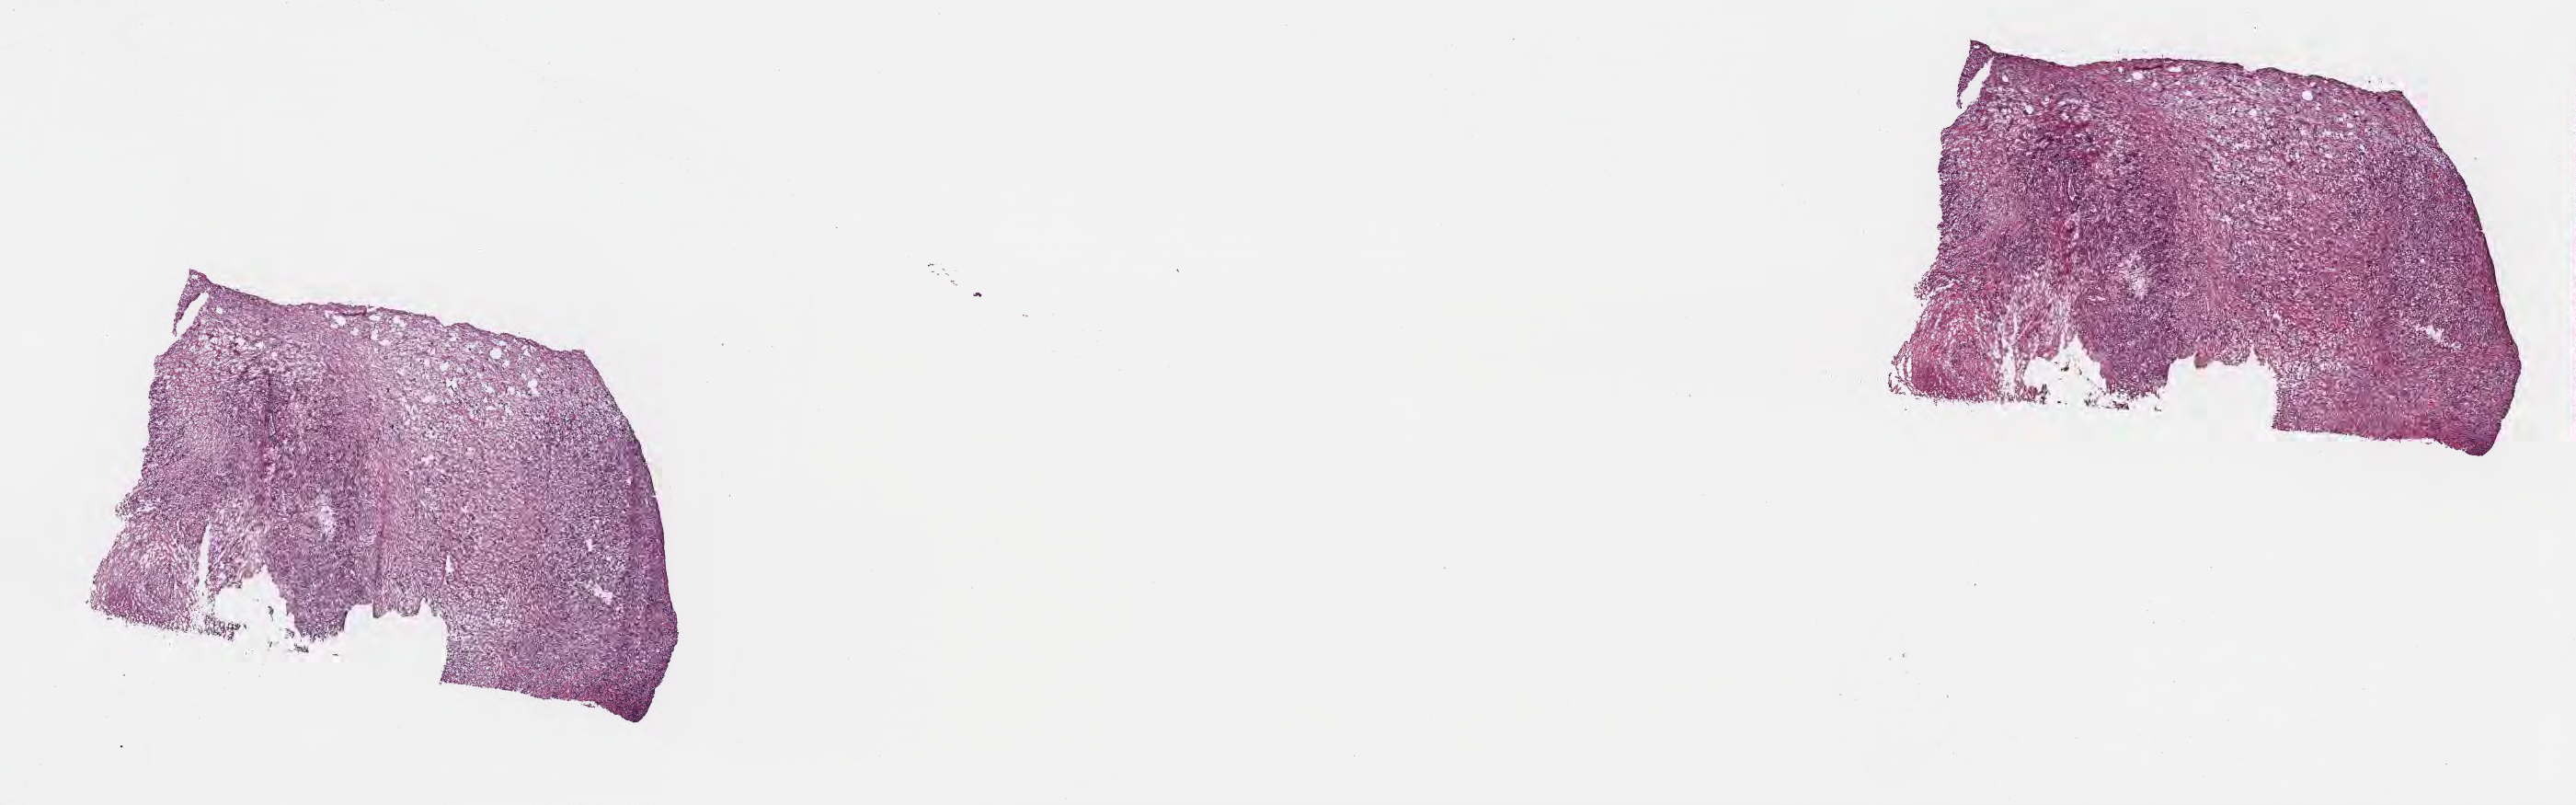
H&E whole-slide image, low-resolution overview of the scanned area, about 22.7 x 7.1 mm. Frozen section (tissue freezing medium). Primary tumor. Anatomic site: tail of pancreas. Patient: female, age at initial diagnosis 71 years. Tumor grade: G3 (poorly differentiated). Composition of this section per pathologist review: tumor cells 50%, tumor nuclei 50%, stromal cells 50%, necrosis 0%, normal cells 0%. Inflammatory infiltration, as recorded: lymphocyte infiltration 0%, monocyte infiltration 0%, neutrophil infiltration 0%.
• section: top of the tissue portion
• AJCC pathologic stage: Stage IA
• diagnosis: Infiltrating duct carcinoma, NOS